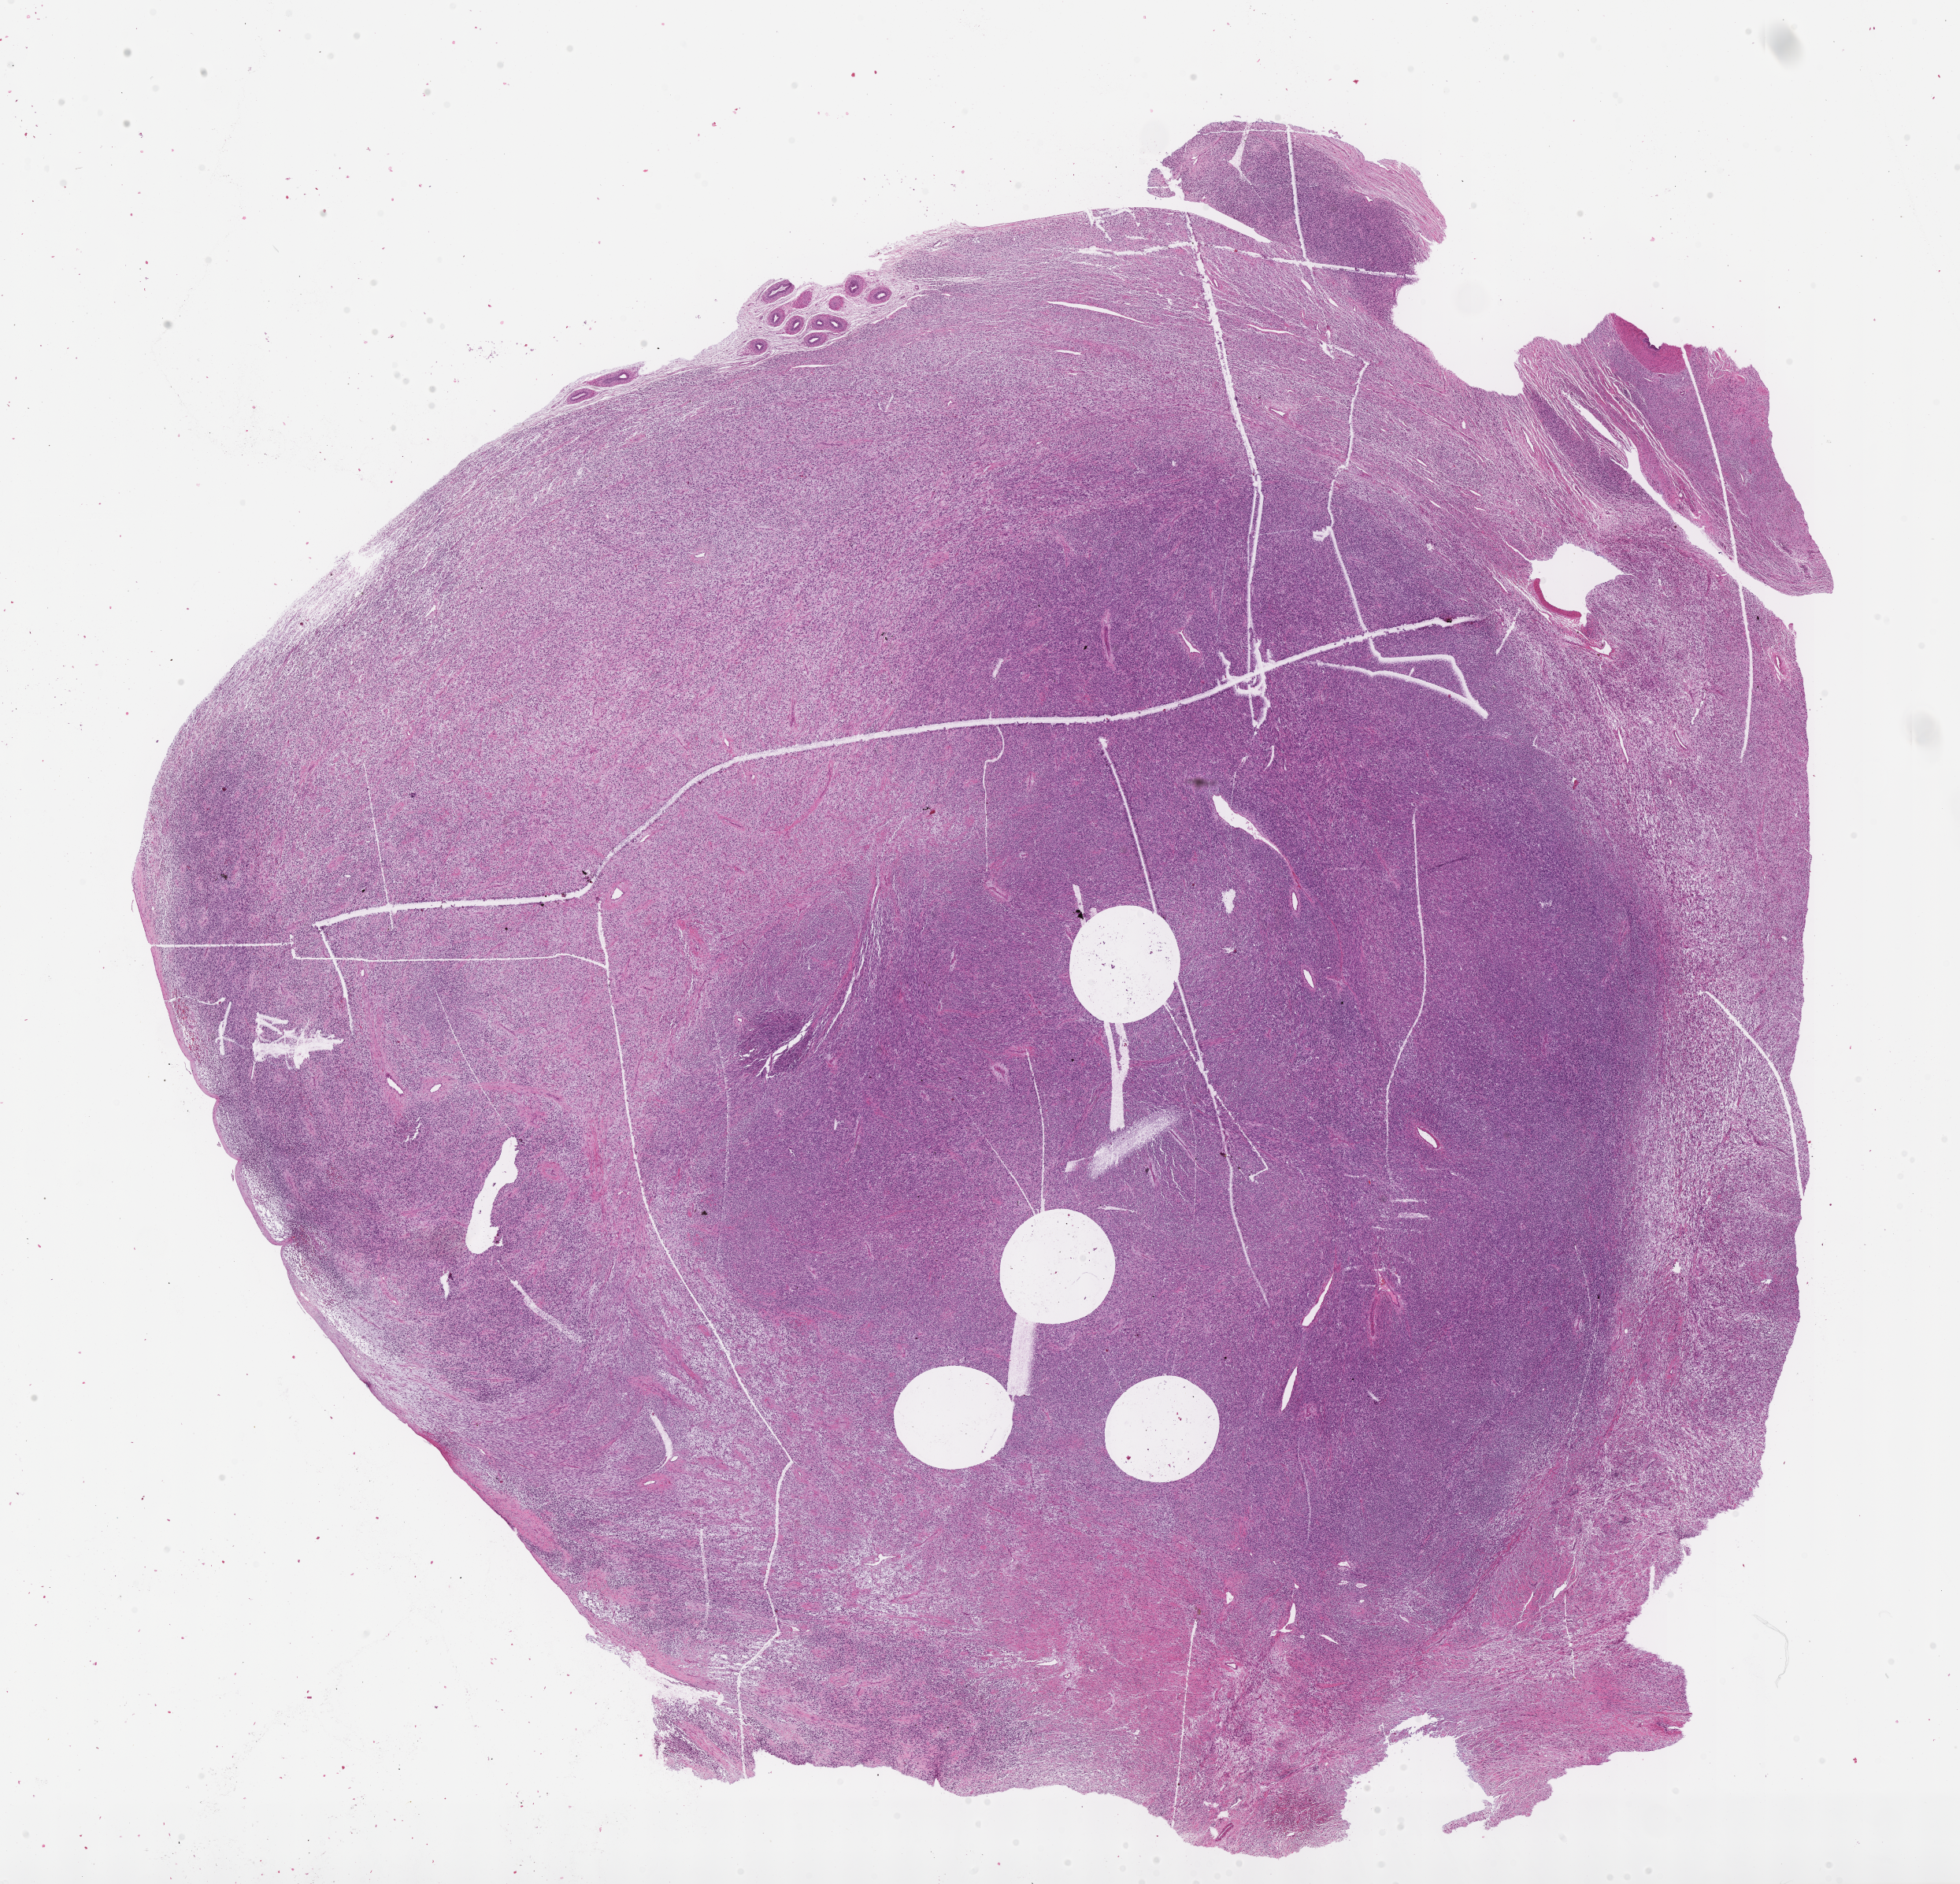
Digitized haematoxylin and eosin-stained section of tumor tissue, whole scanned area (about 20.1 x 19.3 mm) shown as a low-resolution overview, FFPE section, sample anatomic site: testicle, right. Patient: male, age 4.2 years at diagnosis.
Diagnosis: rhabdomyosarcoma; histological classification: embryonal rhabdomyosarcoma. Metastatic status at presentation (as recorded): non-metastatic. Stage (as recorded): 1.